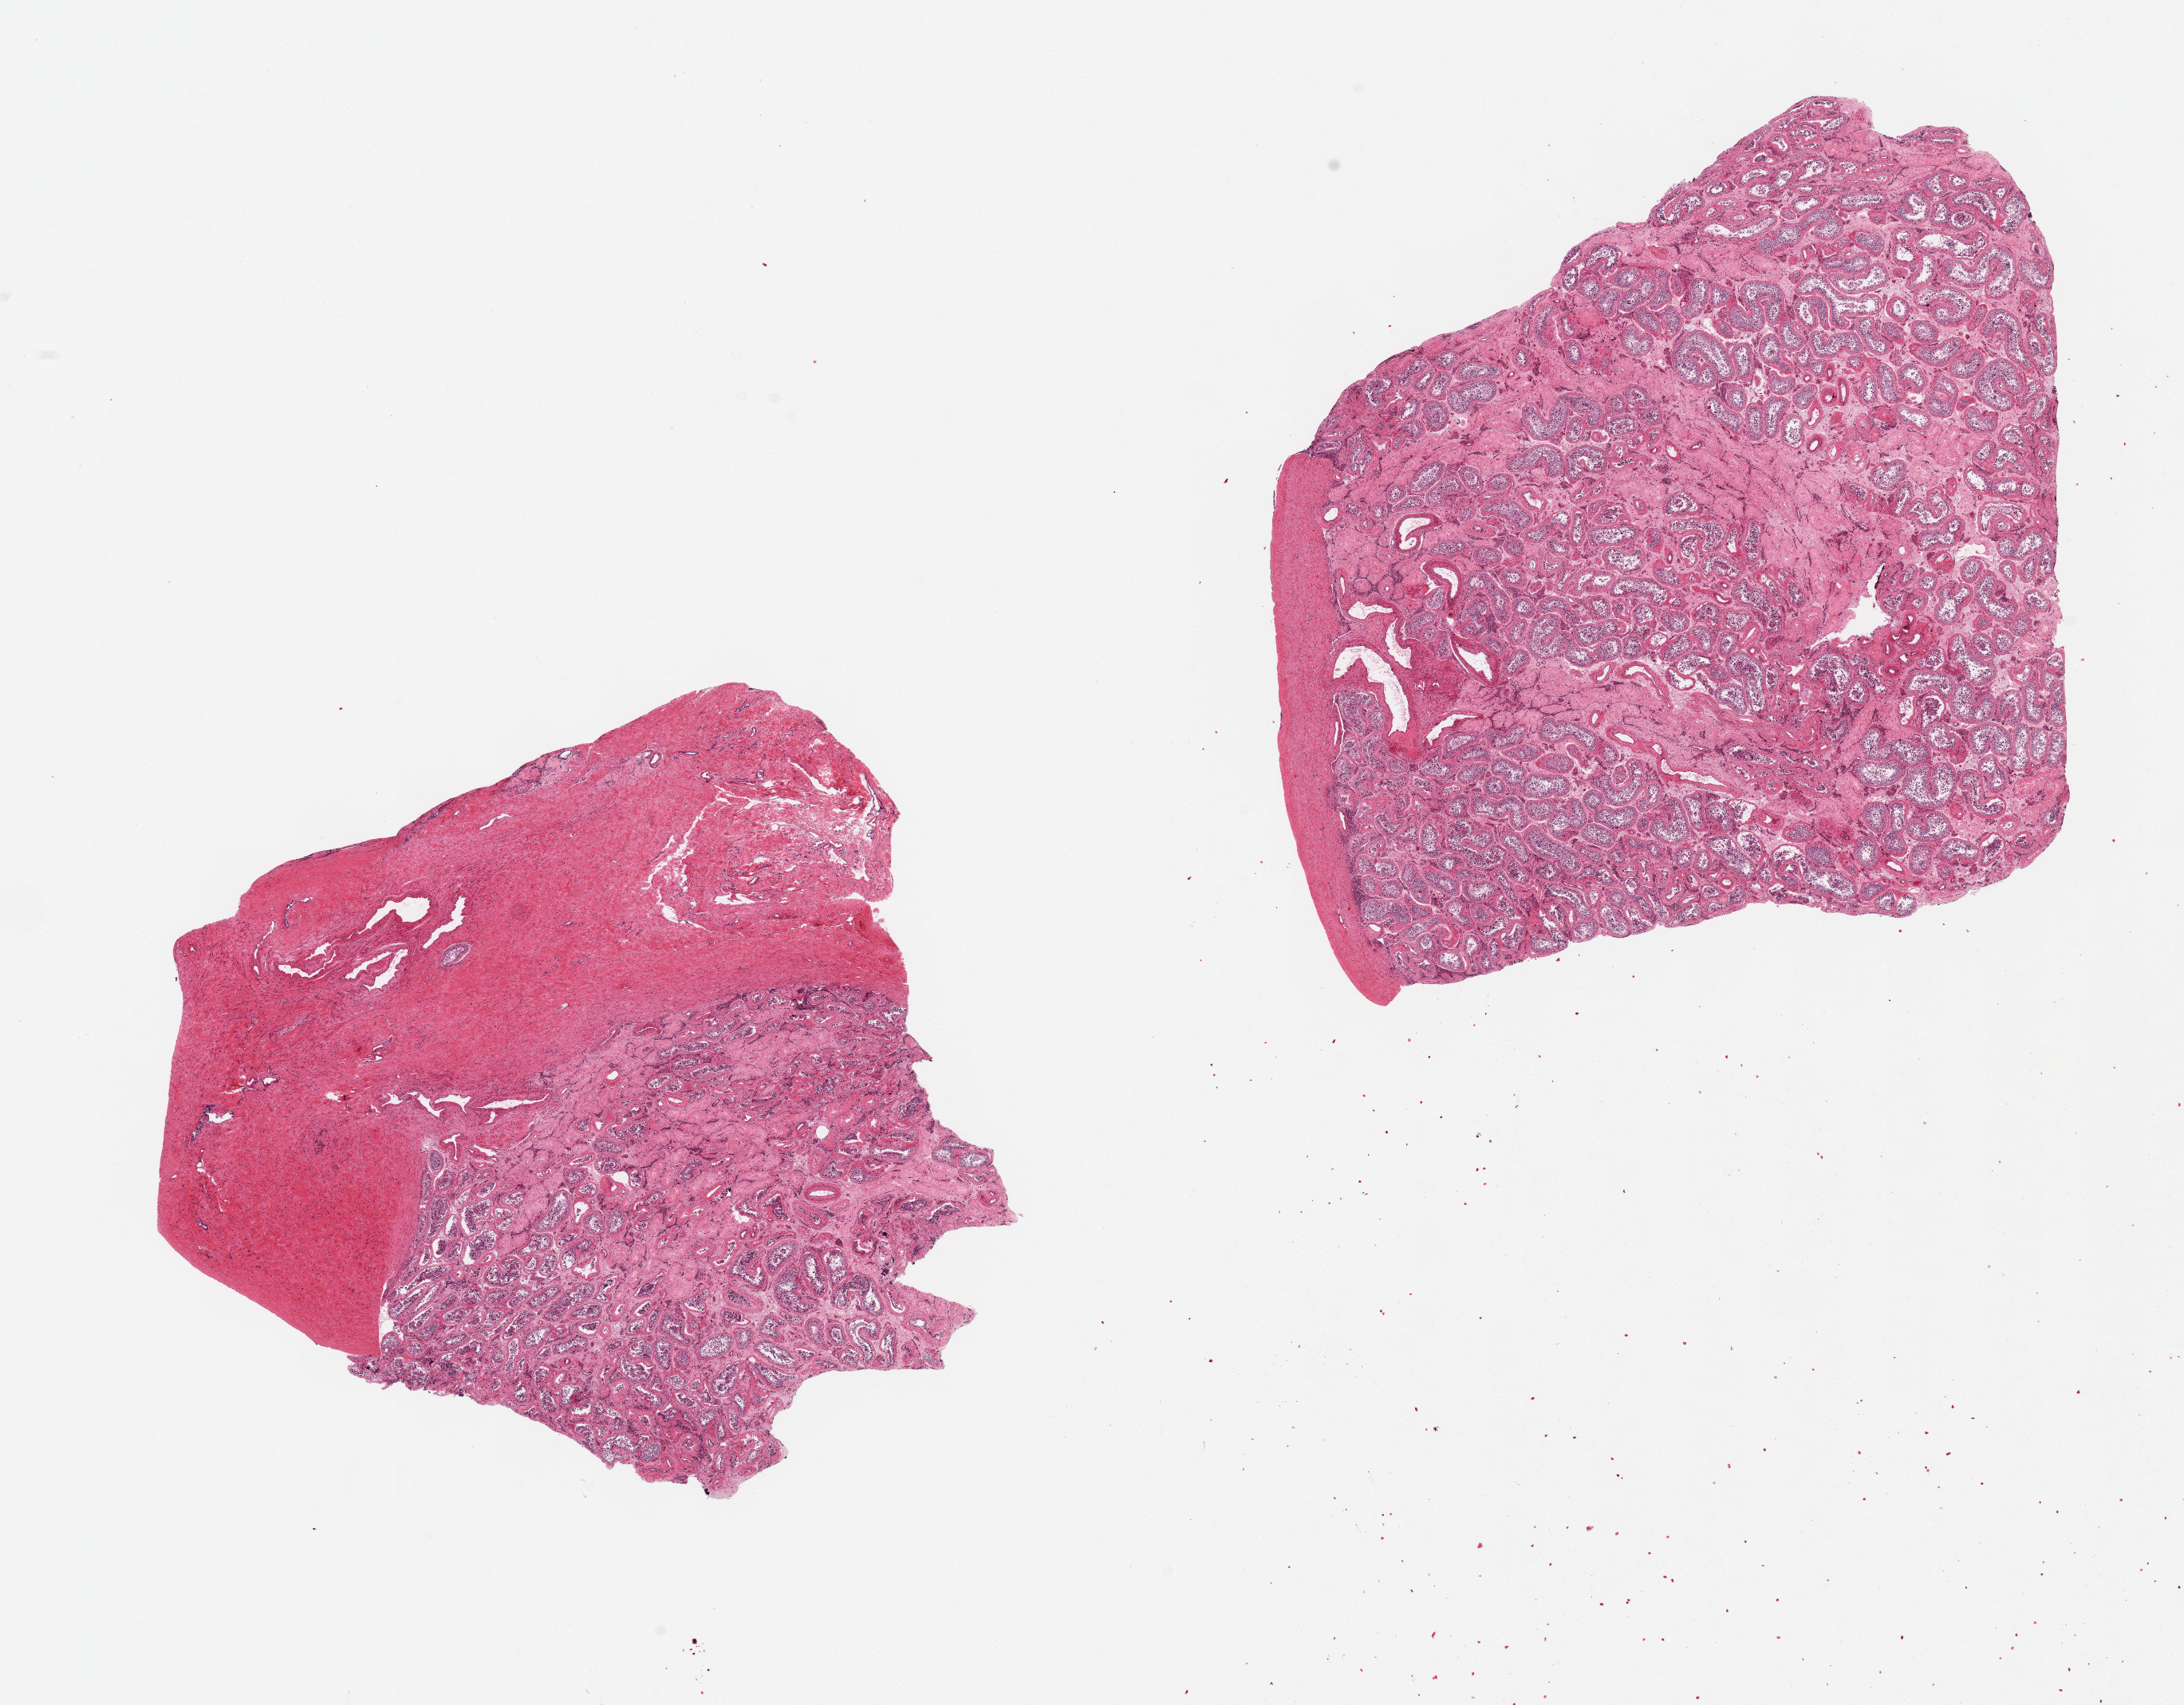
Whole-slide image, H&E stain, low-resolution overview of the scanned area, about 21.7 x 16.9 mm. PAXgene-fixed, paraffin-embedded tissue. Section of testis (target tissue). Donor tissue sample. Male donor.
- review note (as recorded): 2 pieces ~8x8mm, diffuse atrophy/fibrosis, reduced spermatogenesis